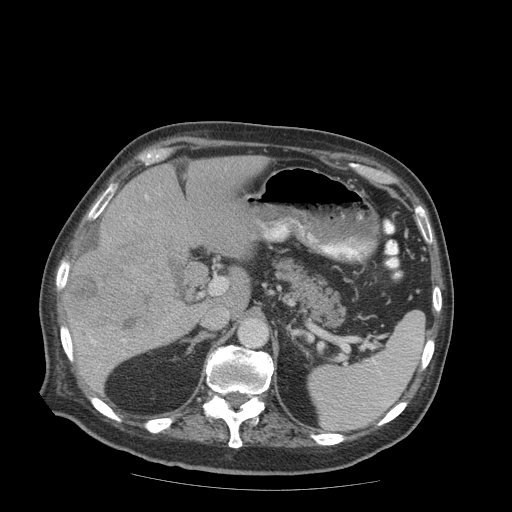
Contrast-enhanced abdominal CT (liver protocol), one axial slice; position 49 of 99 along the scan axis; reconstruction kernel STANDARD; 140 kVp; soft-tissue window (W 400 / L 40 HU); 2.5 mm slice thickness; 512 × 512 image matrix, field of view 420 × 420 mm. From the clinical record (not read from this slice): diagnosis: hepatocellular carcinoma (patient treated with transarterial chemoembolisation; whether this scan precedes or follows treatment is not stated here); TNM stage (as recorded): Stage-IIIB; Child-Pugh class: A; tumour nodularity: multinodular.
Outlined on this slice (semi-automatically segmented with operator editing):
- liver parenchyma outside the tumour (the mass and vessels are separate outlines, so this box may not span the whole liver): bounding box (x1, y1, x2, y2) in pixels: (66, 156, 268, 392)
- mass: (64, 245, 175, 339)
- liver vessels: (91, 339, 125, 344)